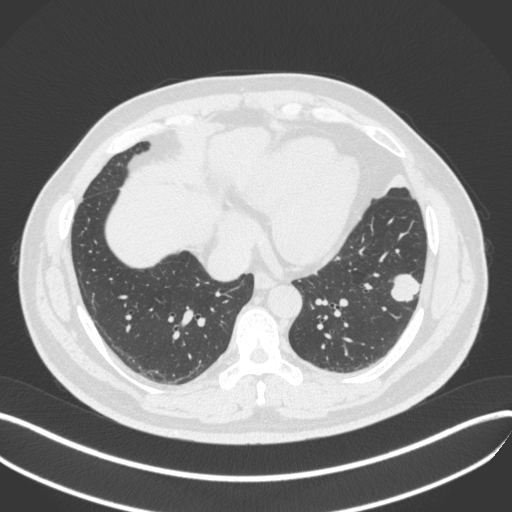
Chest CT, one axial slice; slice 142 of 420 in the series (ordered by position); 120 kVp; lung window (W 1500 / L -600 HU); 1 mm slice thickness; 512 × 512 image matrix, field of view 400 × 400 mm. Patient: male, 39 years. From the clinical record (not read from this slice): clinical TNM (as recorded): T2a N0 M0.
Annotated regions visible in this slice (bounding box drawn by a radiologist):
- lung tumour (recorded histology: adenocarcinoma): bounding box (x1, y1, x2, y2) in pixels: (388, 269, 423, 304)